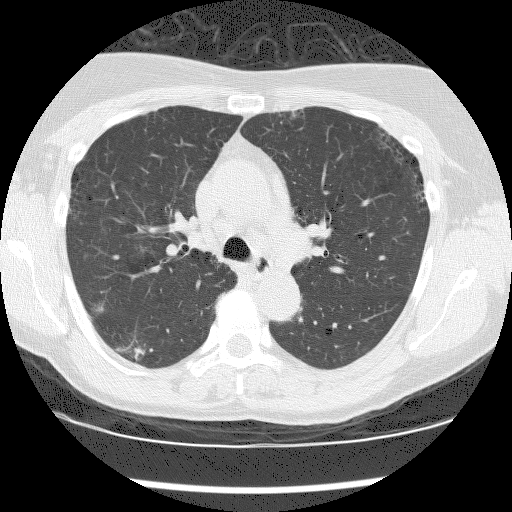
Low-dose screening chest CT, one axial slice. Slice 123 of 176 in the series (ordered by position). 120 kVp. Lung window (W 1500 / L -600 HU). 2.5 mm slice thickness. 512 × 512 image matrix, field of view 320 × 320 mm.
Annotated regions visible in this slice (manually delineated by an expert):
- lesion 1 (tumor, lower lobe of right lung): box from (x=134, y=347) to (x=145, y=360) px